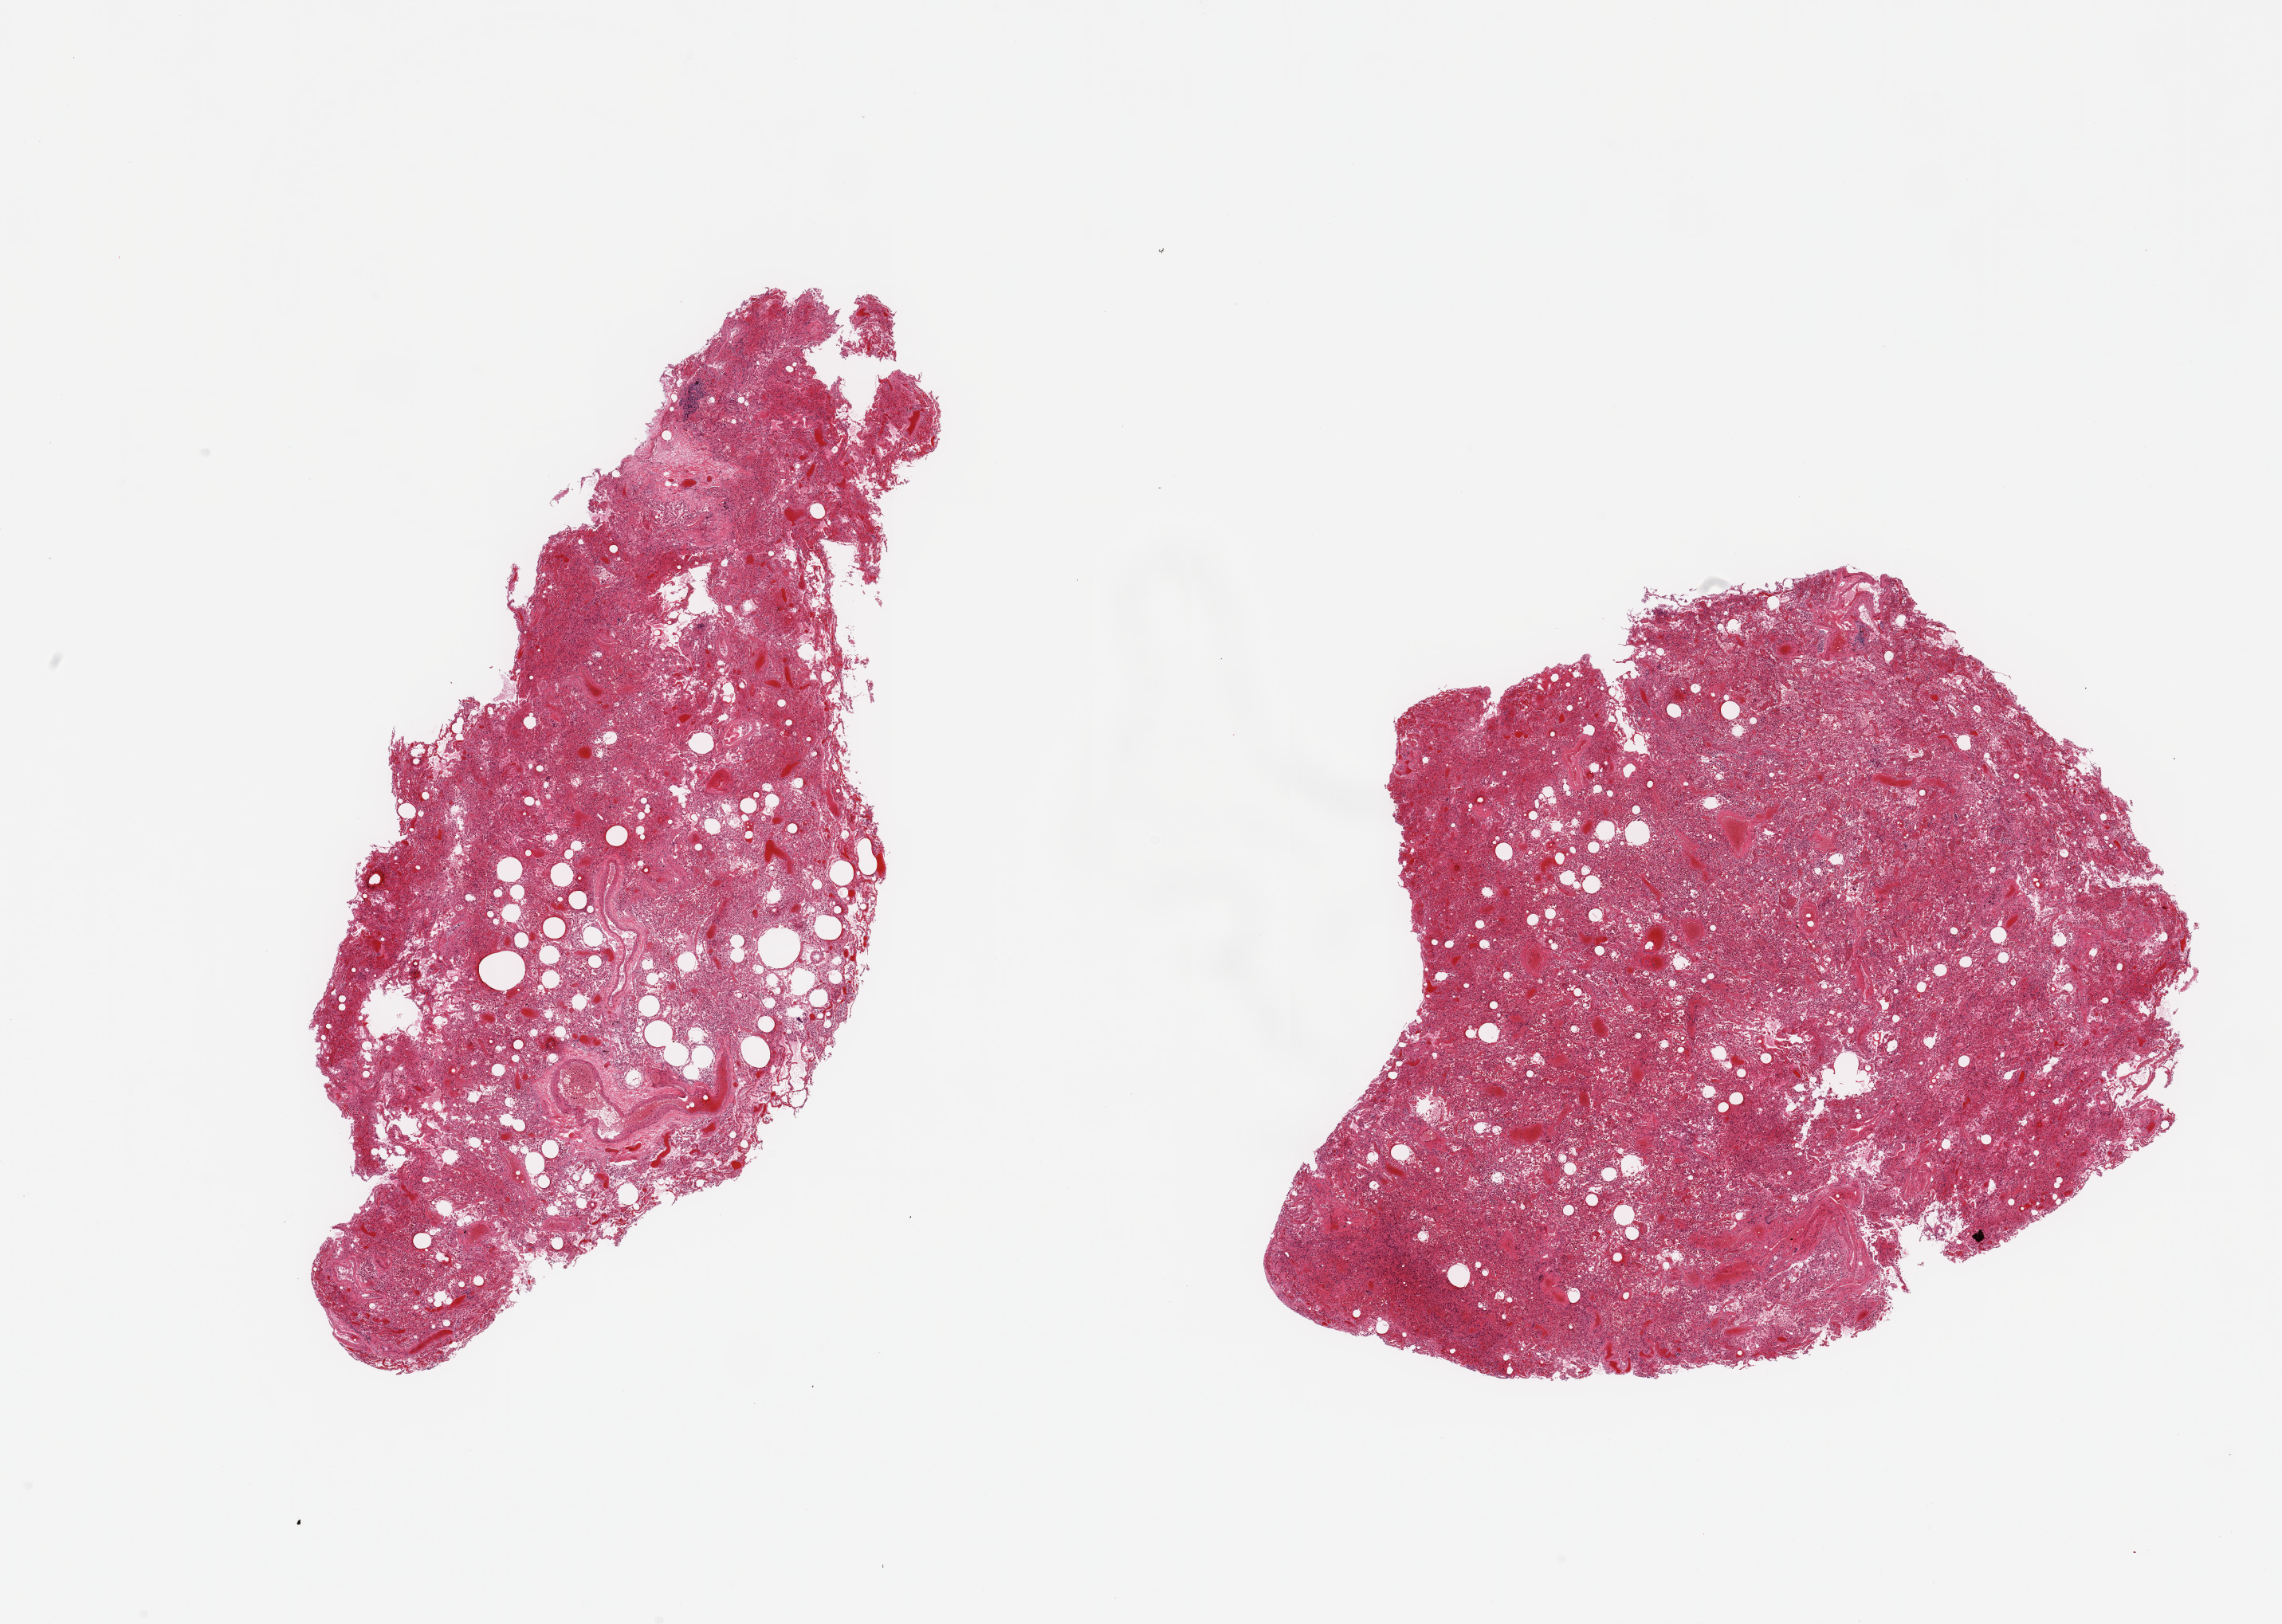
Digitized haematoxylin and eosin-stained section — whole scanned area (about 22.6 x 16.1 mm, acquisition: 20x scan) shown as a low-resolution overview; PAXgene-fixed paraffin-embedded (PFPE) section; sampled site (target tissue): lung; tissue donor sample.
• review note (as recorded): 2 pieces; severe congestion, edema, atelectasis